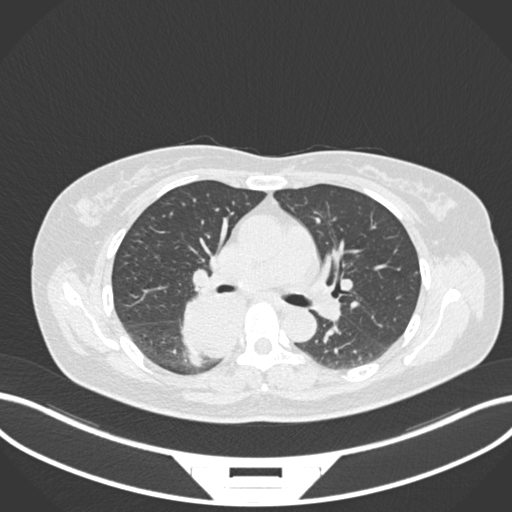
Chest CT, one axial slice; lung window (W 1500 / L -600 HU); 512 × 512 image matrix, field of view 400 × 400 mm. Patient: female, 54 years. From the clinical record (not read from this slice): clinical TNM (as recorded): T4 N0 M0.
Outlined on this slice (bounding box drawn by a radiologist):
- lung tumour (recorded histology: adenocarcinoma): box from (x=179, y=286) to (x=253, y=363) px